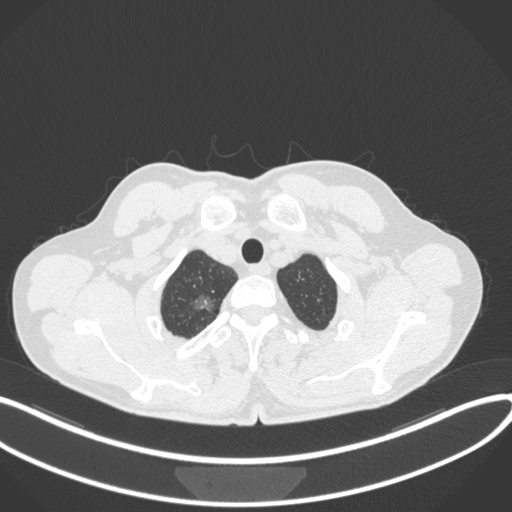
Chest CT, one axial slice. Position 350 of 407 along the scan axis. Reconstruction kernel B31f. 120 kVp. Lung window (W 1500 / L -600 HU). 1 mm slice thickness. 512 × 512 image matrix, field of view 400 × 400 mm. Male patient, age 58 years. Case-level facts recorded for this patient, not image findings: clinical TNM (as recorded): T1c N0 M0.
Structures marked on this image (bounding box drawn by a radiologist):
- lung tumour (recorded histology: adenocarcinoma): bounding box [x1, y1, x2, y2] px = [186, 286, 214, 317]